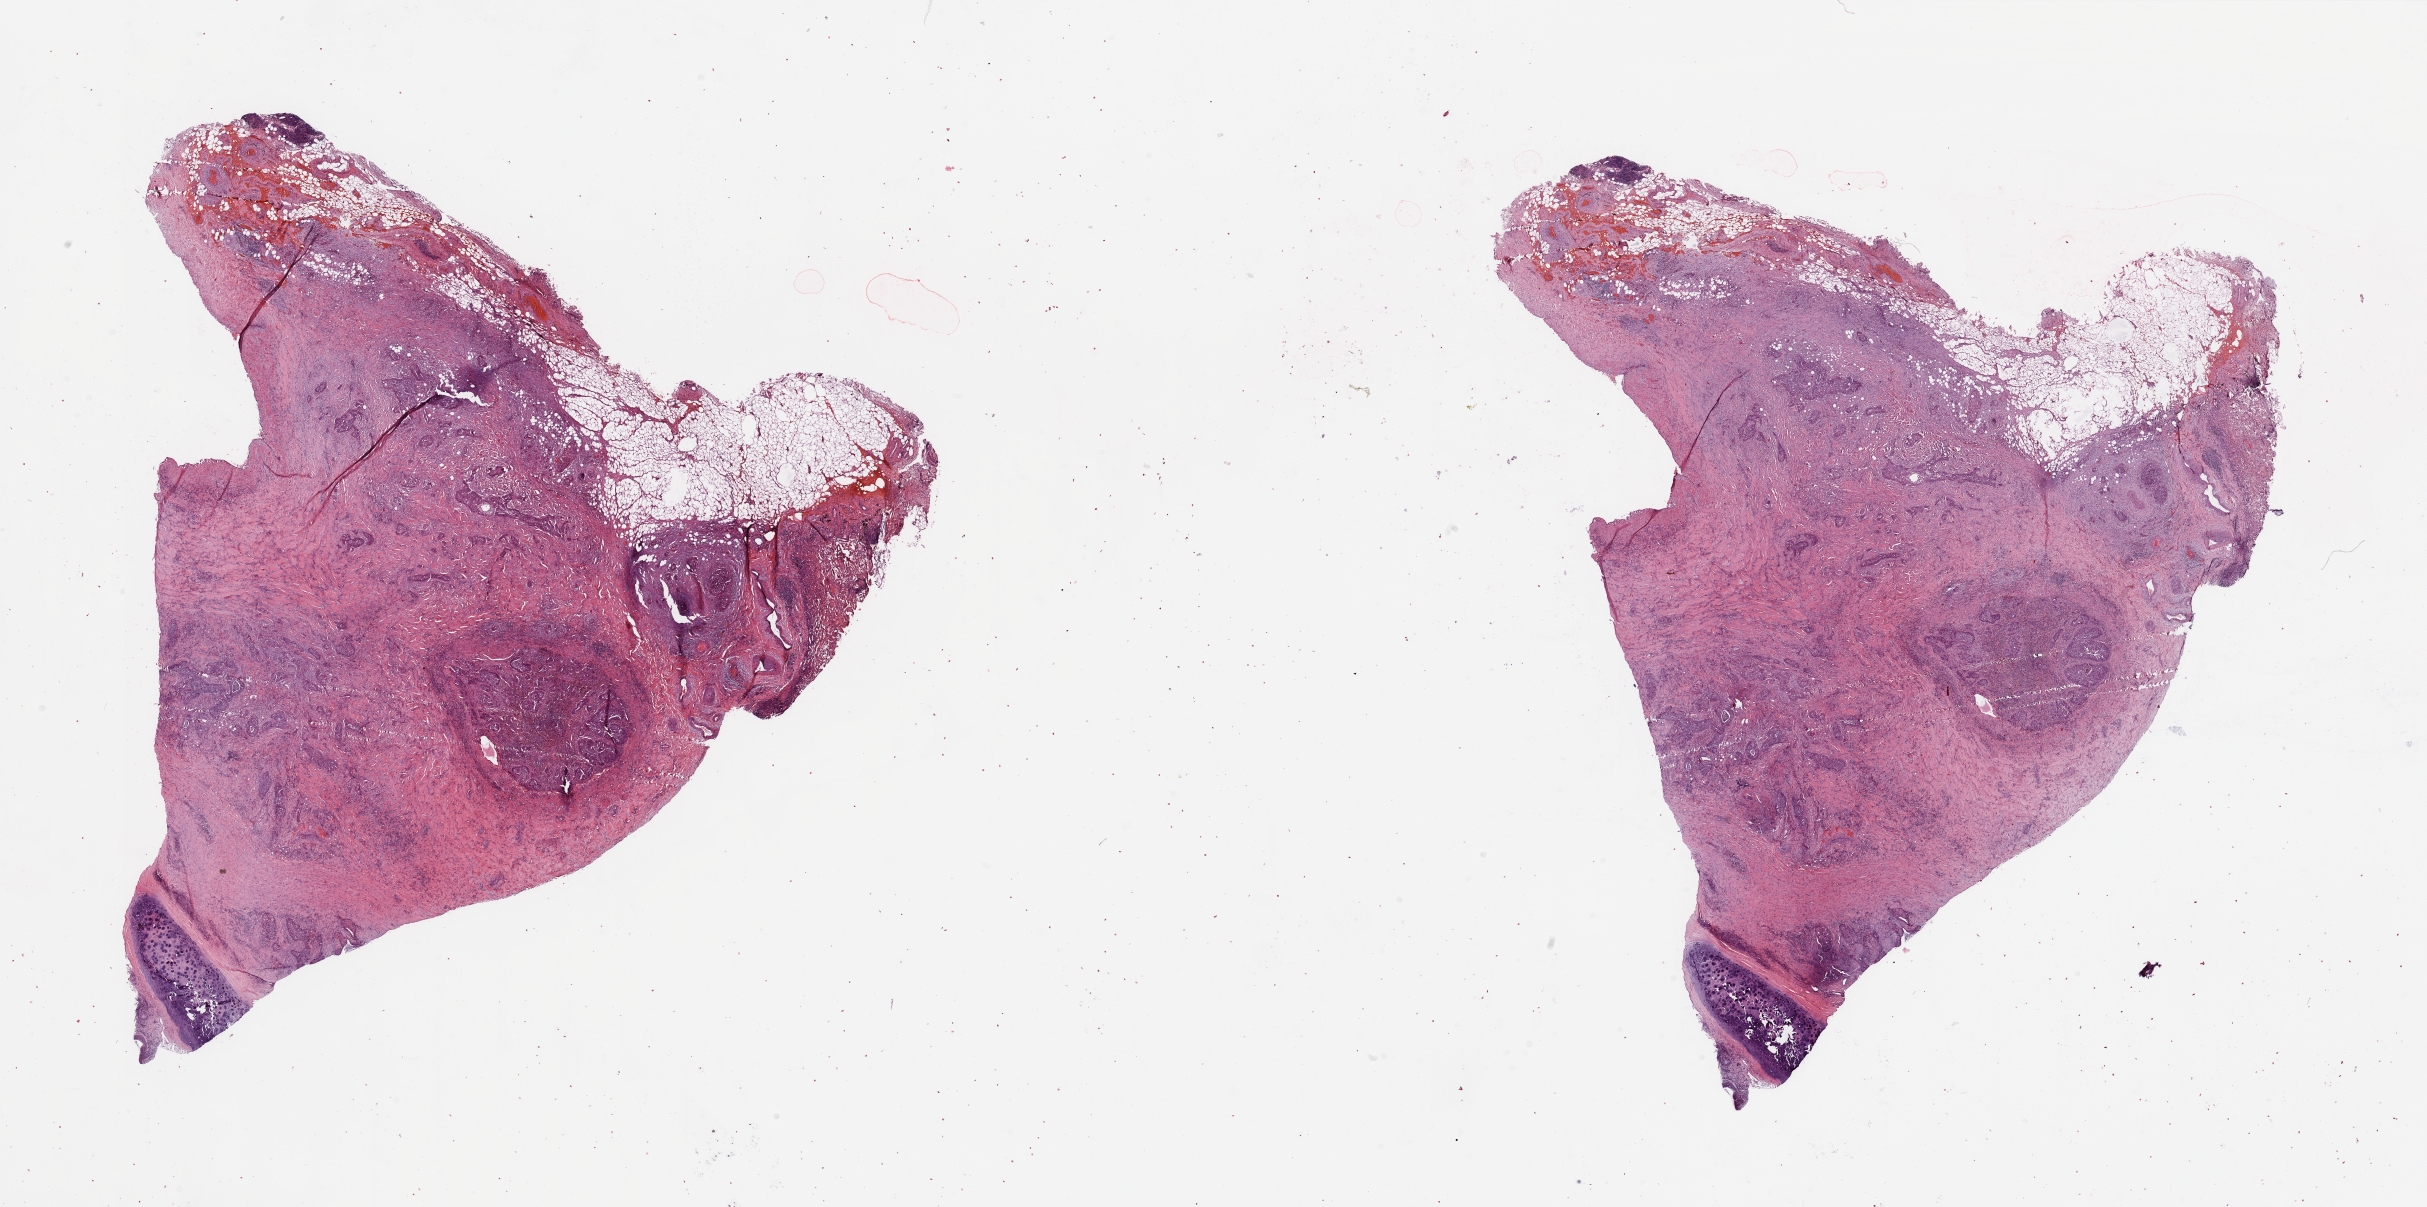
Digitized H&E-stained tissue section (whole slide), low-resolution overview of the scanned area, about 38.4 x 19.1 mm (from a 20x scan). Lung, tumour tissue. 72-year-old male patient. Histologic grade: G3 (poorly differentiated).
Diagnosis: Squamous cell carcinoma, NOS. AJCC pathologic stage: IIA.